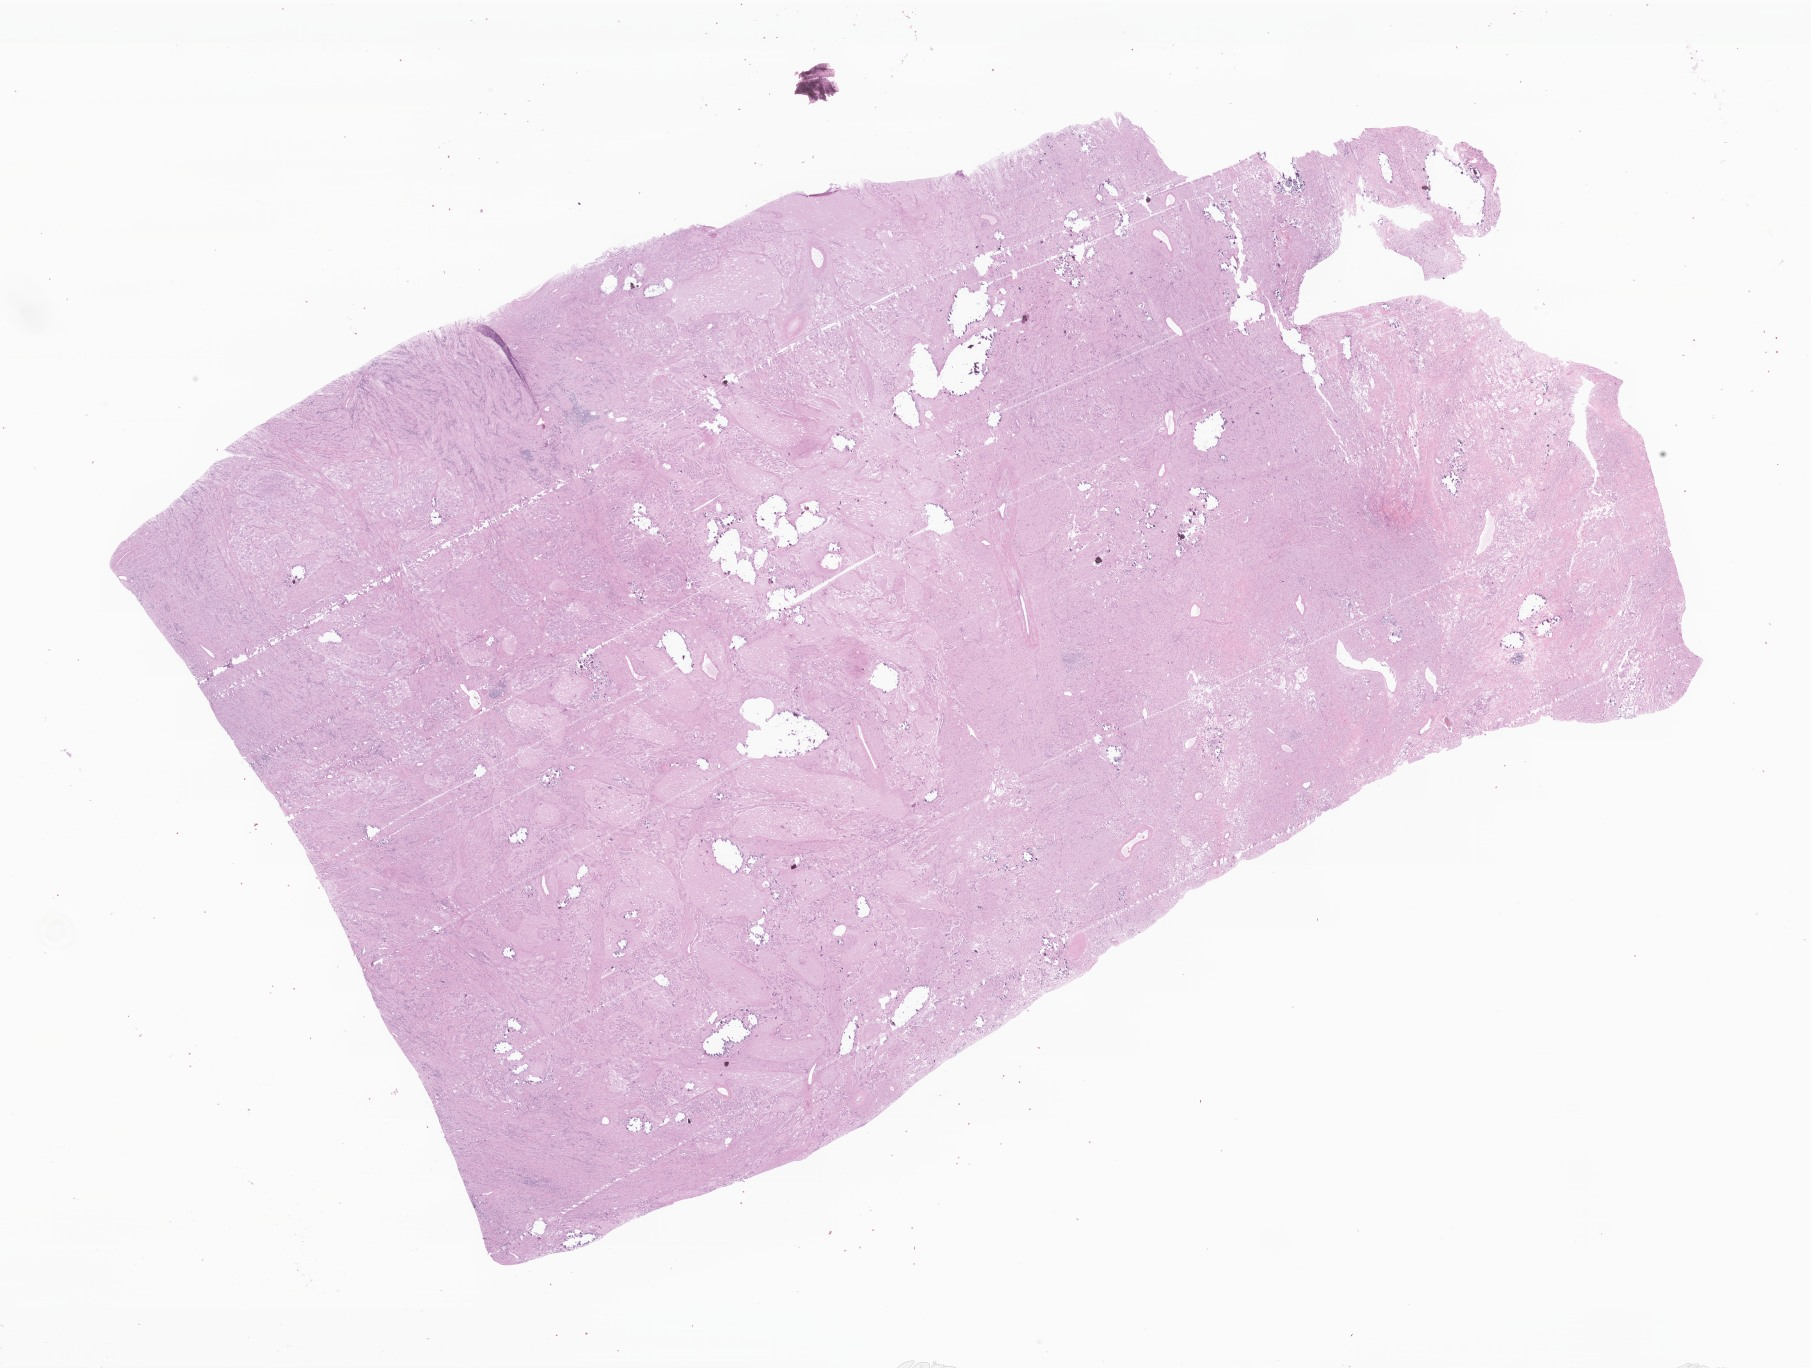
Whole-slide image, haematoxylin and eosin stain of tumor tissue from the adrenal gland, whole scanned area (about 30.6 x 23.1 mm) shown as a low-resolution overview; FFPE section. Patient female; age 95 months.
Recorded diagnosis: Neuroblastoma, NOS.